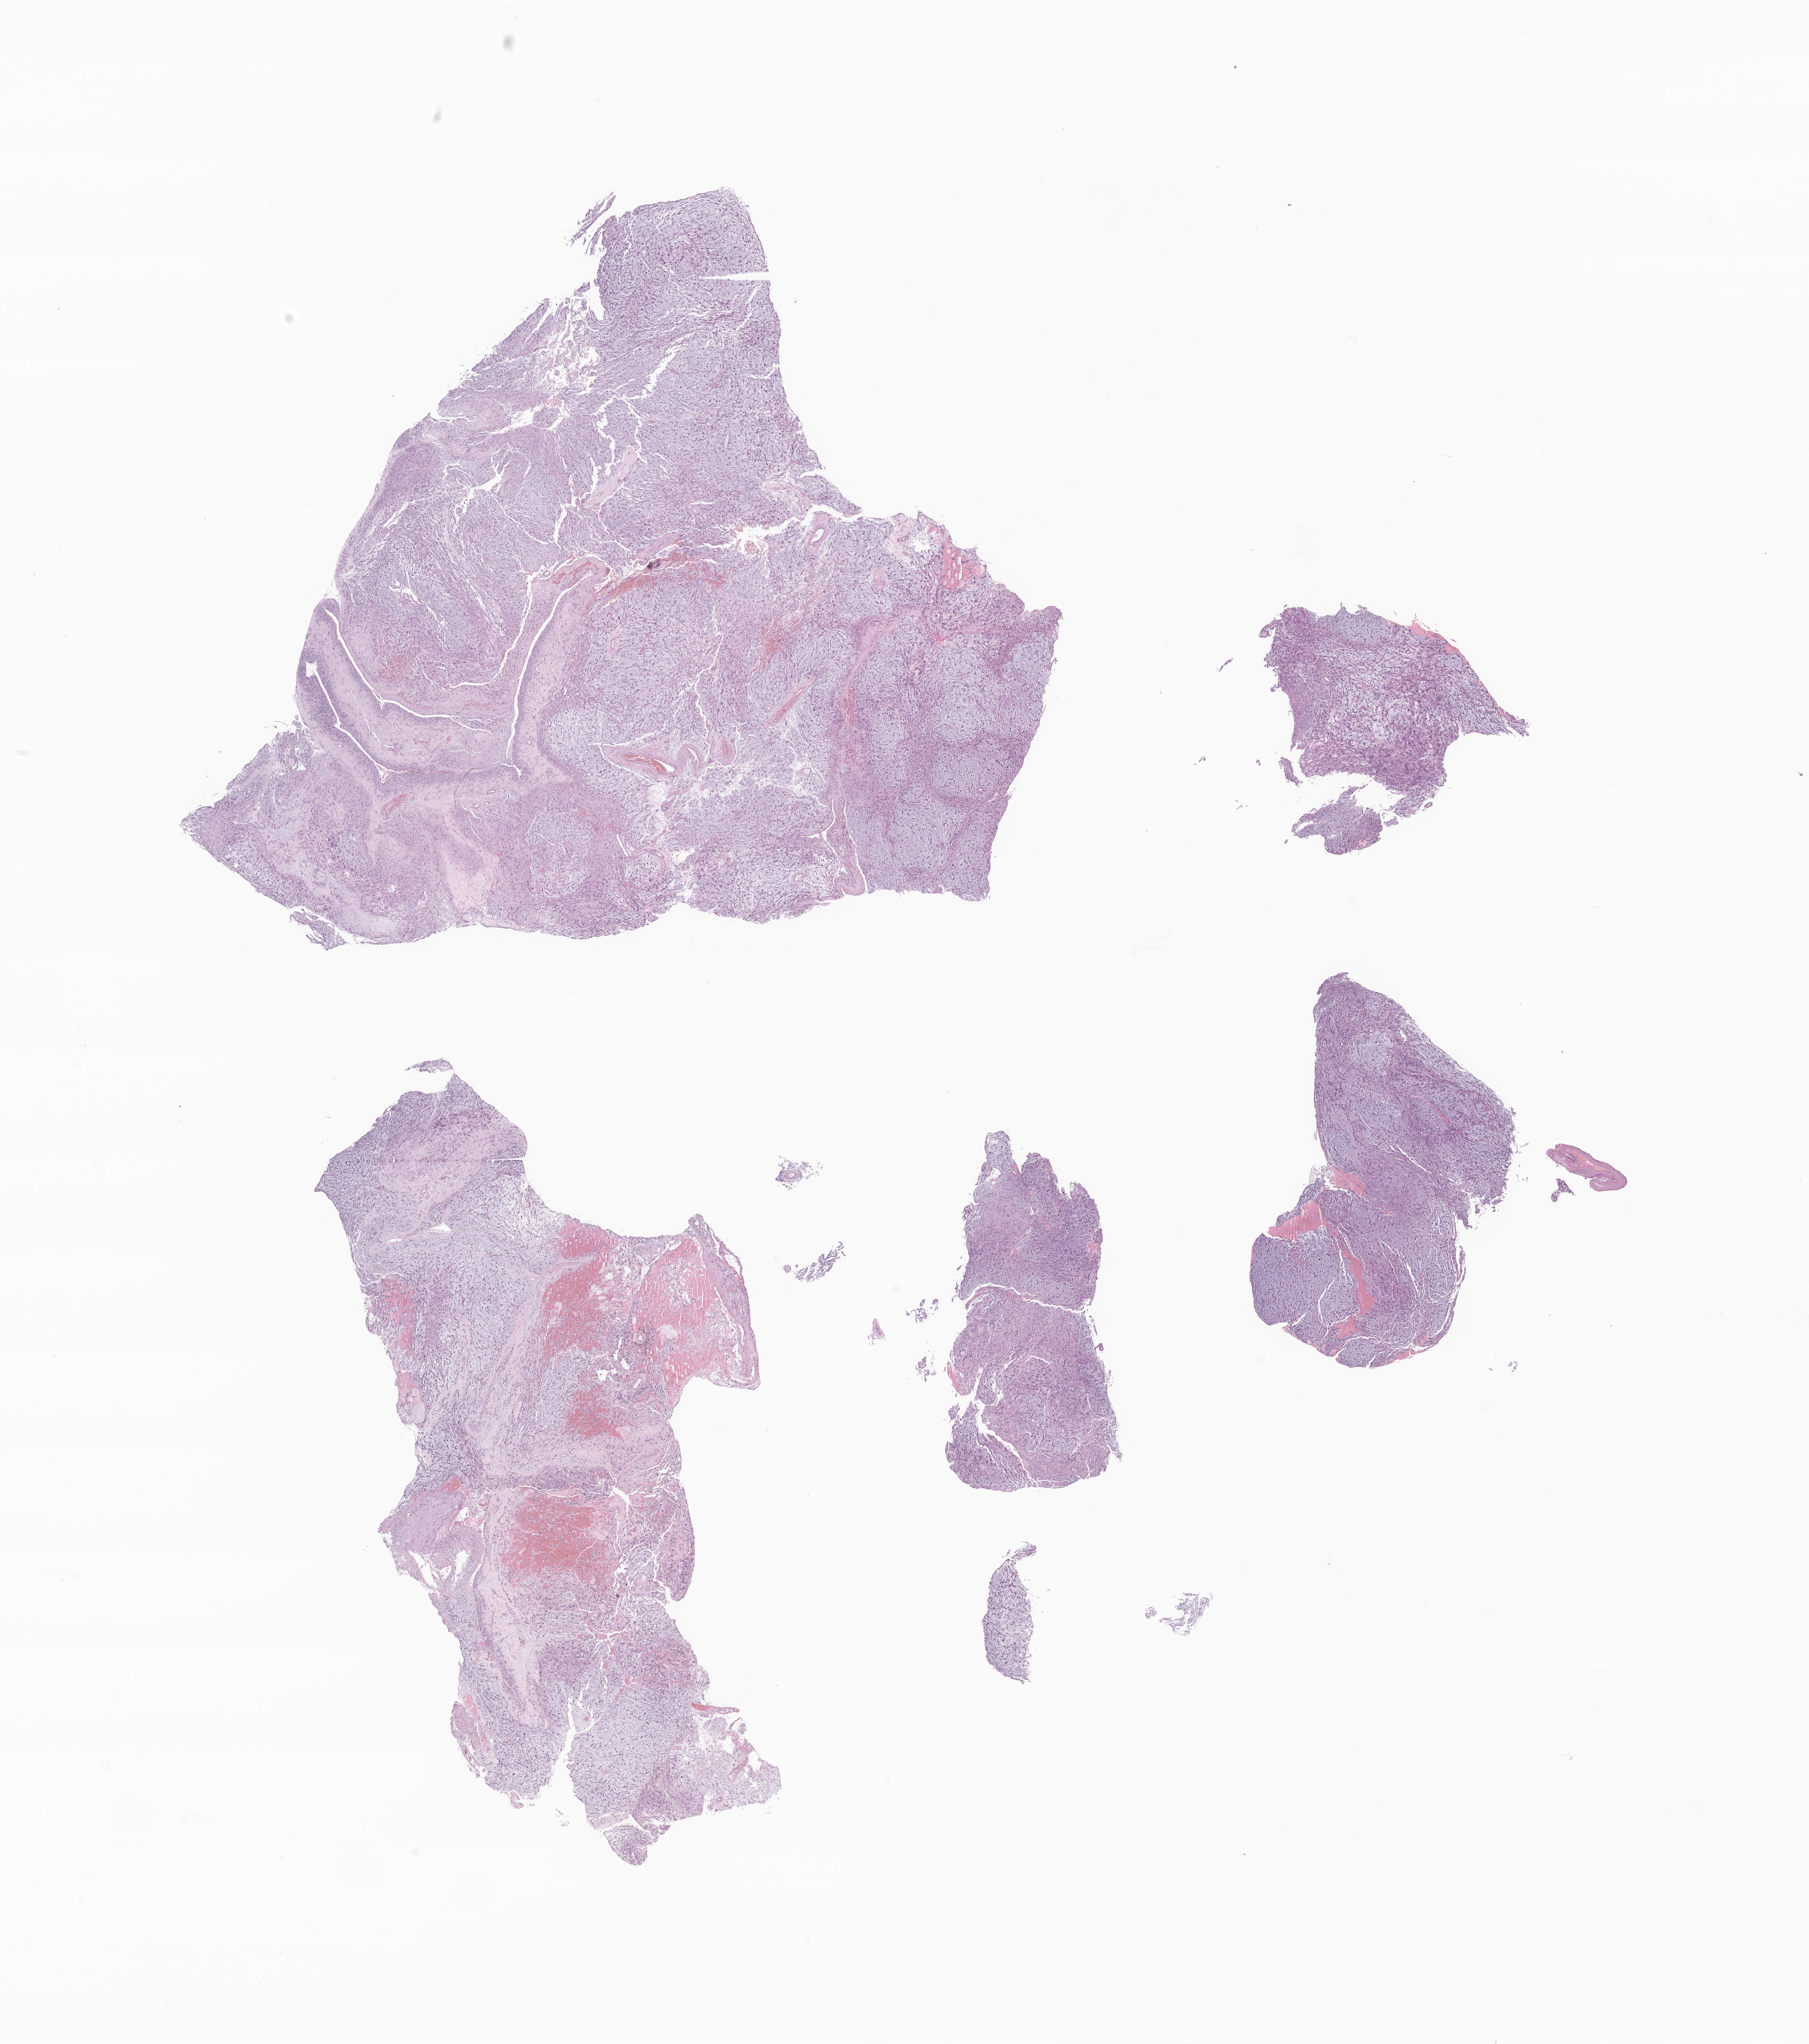
Haematoxylin and eosin whole-slide image of tumor tissue from the frontal lobe — low-resolution overview of the scanned area, about 19.4 x 21.9 mm, FFPE section. Male patient, age 67 months (5 years 7 months).
• diagnosis (ICD-O-3 morphology term): Glioma, malignant